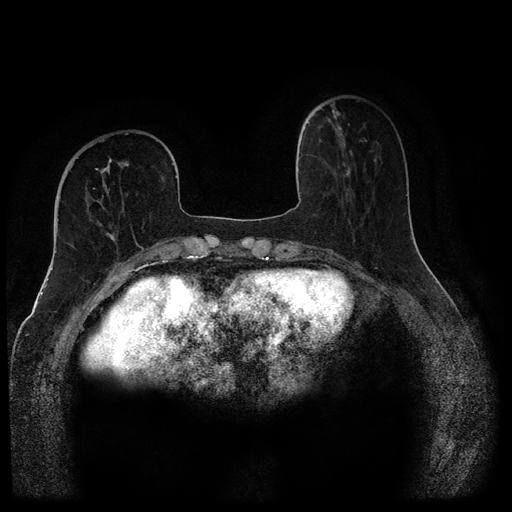
Breast MRI (dynamic contrast-enhanced, multi-phase), one axial slice. Position 35 of 116 along the scan axis. Dynamic contrast-enhanced series, time point 2 of 5 at this slice position (early post-contrast). 1.5 T. TE 2.6 ms, TR 5.4 ms. 2 mm slice thickness. 512 × 512 image matrix, field of view 340 × 340 mm. Female patient, age 68 years.
Structures marked on this image (semi-automatically segmented with operator editing):
- breast lesion (labelled benign in the annotation): bounding box <328,105,350,134> (left, top, right, bottom; pixels)